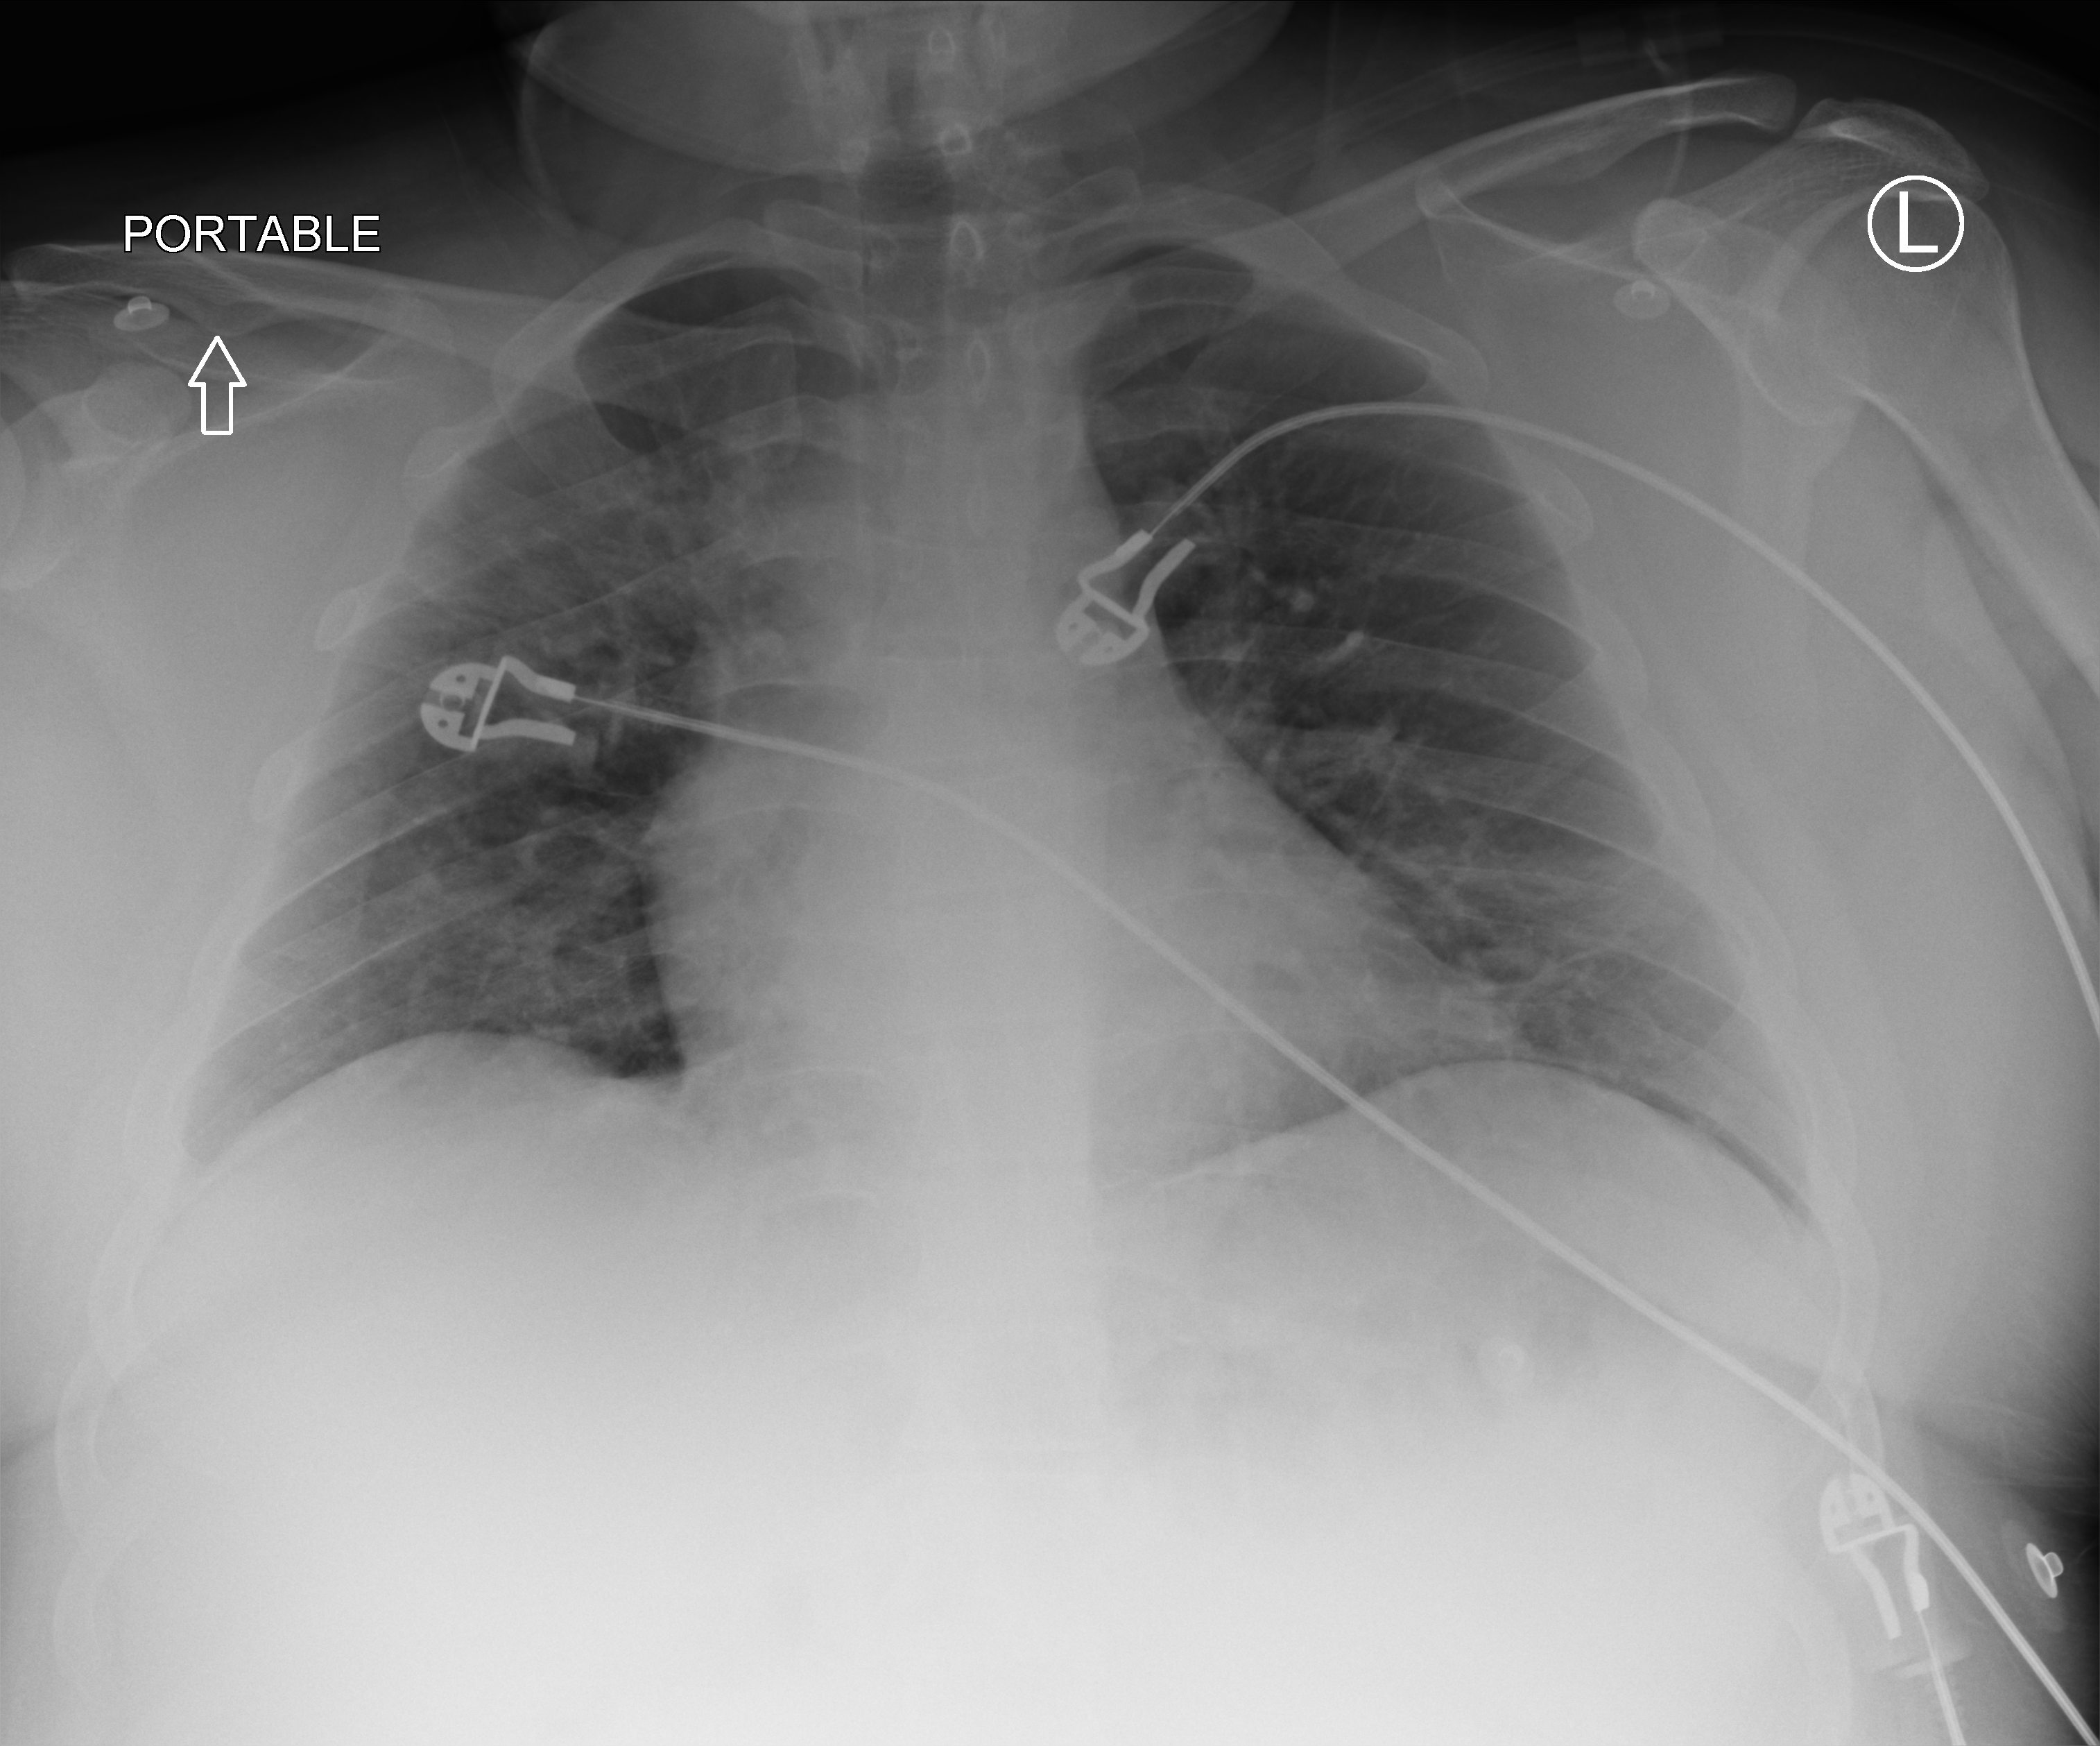
Portable chest radiograph, anteroposterior (AP) projection. Patient hospitalised with COVID-19; male, aged 18–59 years.
Hospital-stay facts (about this admission, not read from this image; timing relative to this image not recorded):
- length of hospital stay: 7 days
- COPD (admission record): no